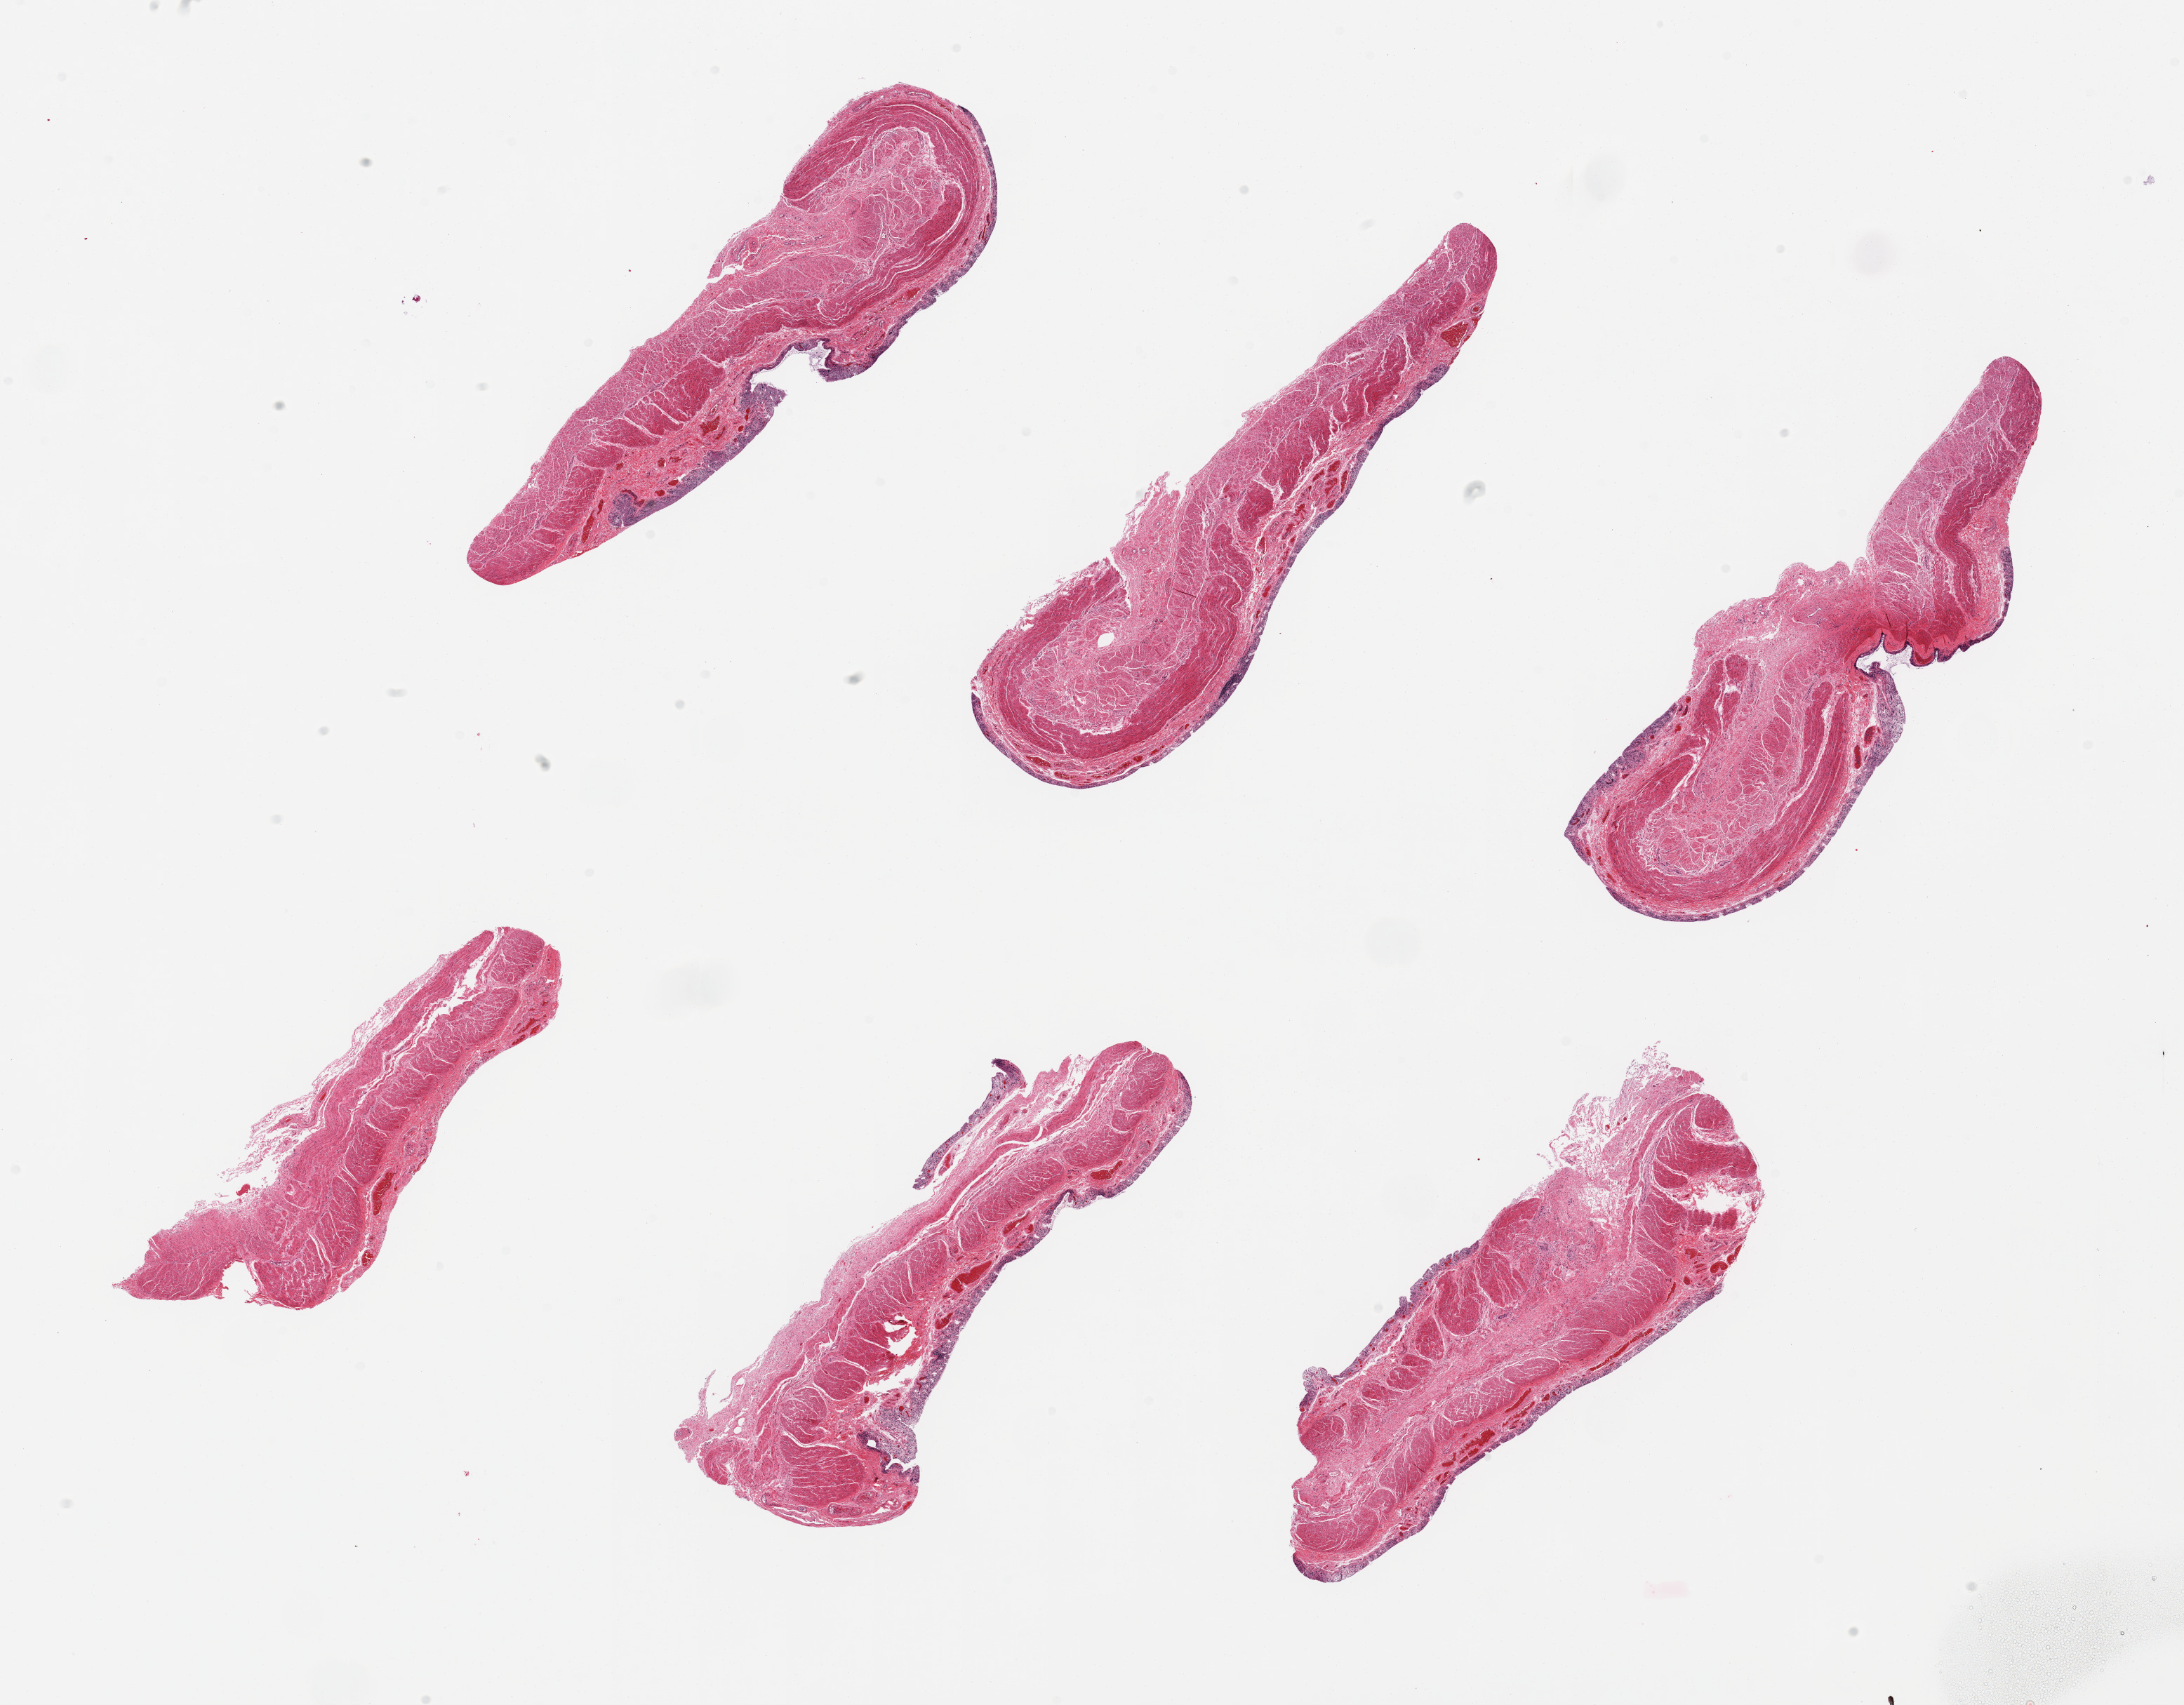
Digitized hematoxylin and eosin (H&E)-stained section — whole scanned area (about 24.6 x 19.2 mm) shown as a low-resolution overview. PAXgene-fixed, paraffin-embedded tissue. Target tissue: transverse colon. Donor tissue sample. Donor sex: male.
• pathologist's review note for this sample: 6 pieces, mucosa totally autolyzed/sloughed